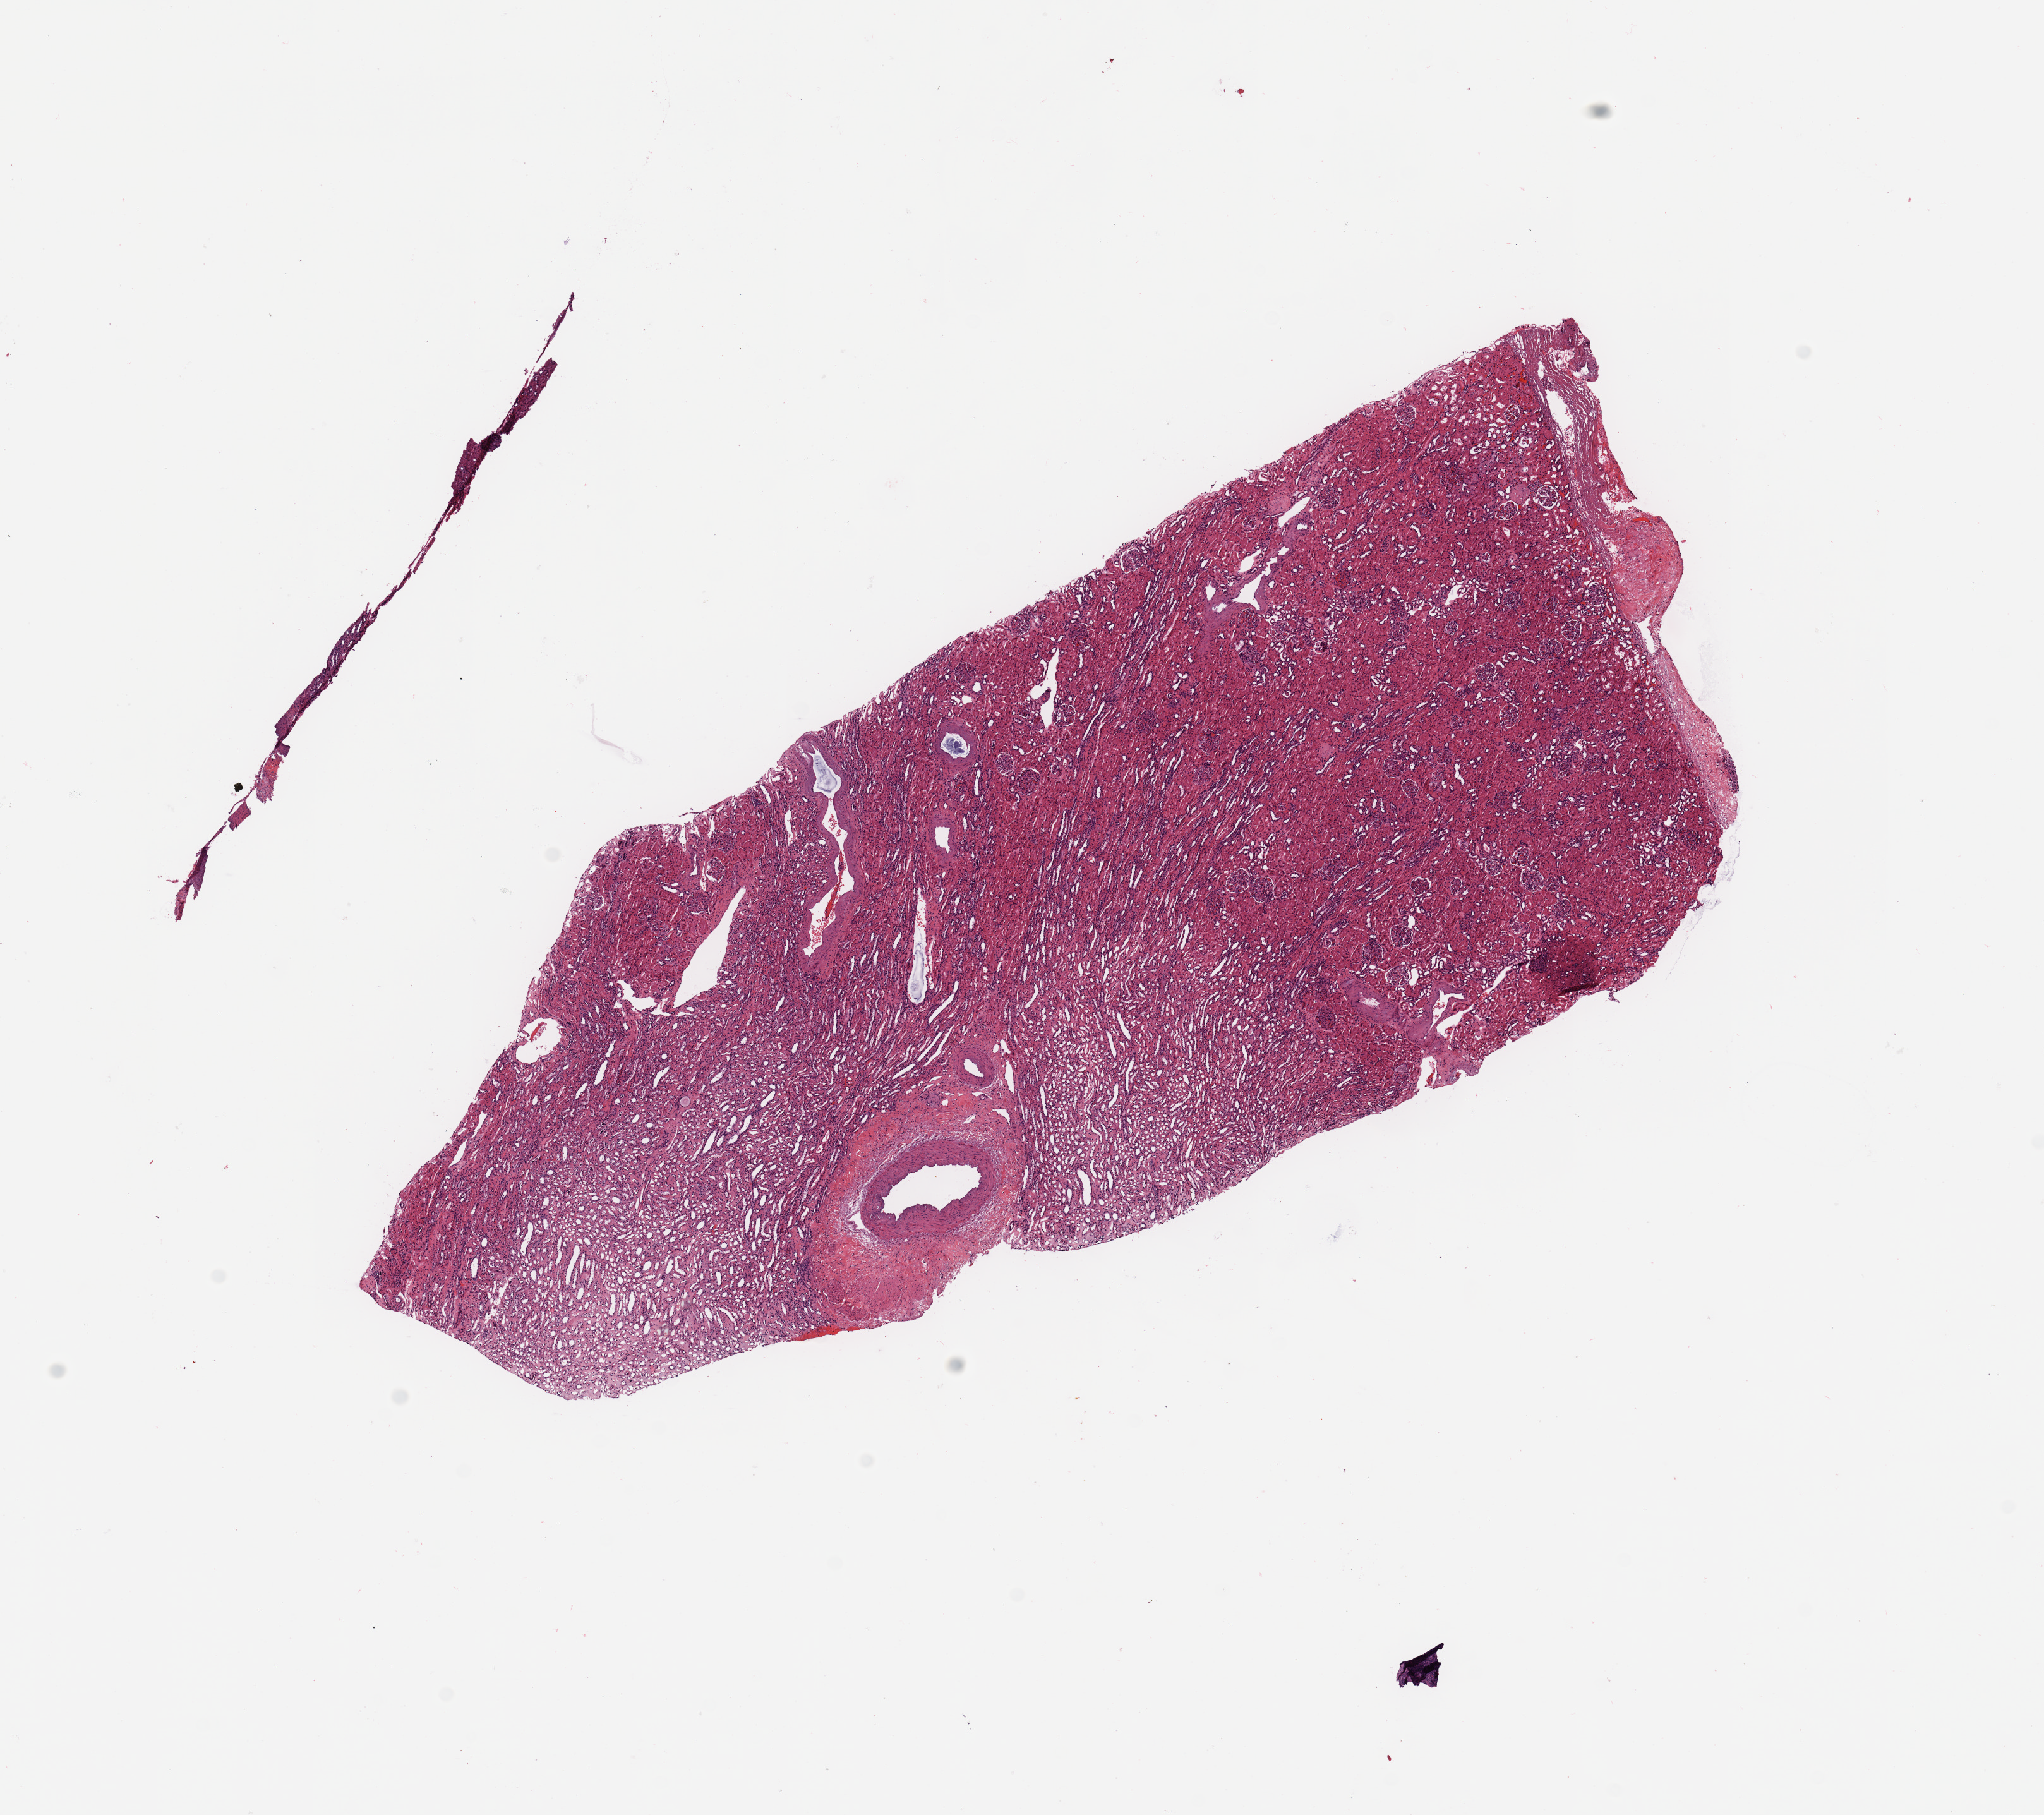
Digitized H&E-stained tissue section (whole slide), whole scanned area (about 12.8 x 11.4 mm, from a 20x scan) shown as a low-resolution overview; normal (non-tumour) tissue sample, kidney. Female, 57 y/o.
This section: normal (non-tumour) tissue from the same patient. Patient diagnosis: Renal cell carcinoma, NOS.